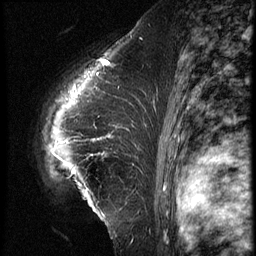
Breast MRI (dynamic contrast-enhanced), one sagittal slice; position 45 of 62 along the scan axis; 3 images stored at this slice position (order not interpretable as contrast timing); 1.5 T; TE 4.2 ms, TR 9 ms; 2.5 mm slice thickness; 256 × 256 image matrix. Female patient, age 39 years. From the clinical record (not read from this slice): setting: breast cancer imaged before/during neoadjuvant chemotherapy; receptor status: HER2-positive.
Structures marked on this image (semi-automatically segmented with operator editing):
- analysis volume of interest (the breast-tissue region the enhancement analysis was run in; not a lesion): bounding box [x1, y1, x2, y2] px = [34, 64, 152, 228]
- tumour enhancement mask (voxels above the 140 % enhancement threshold inside the analysis volume of interest): [109, 134, 111, 137]